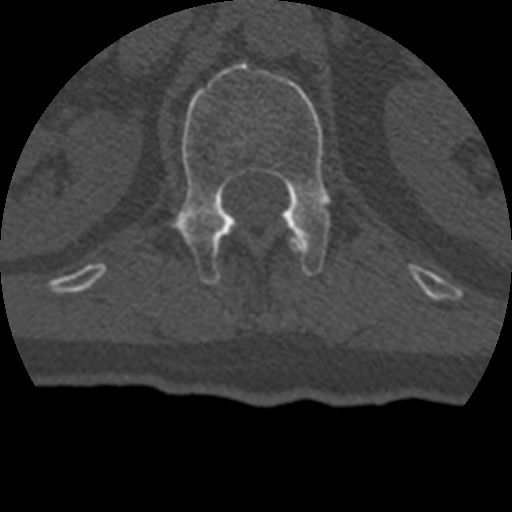
CT including the spine, one axial slice; slice 153 of 399 in the series (ordered by position); reconstruction kernel STANDARD; 120 kVp; bone window (W 1800 / L 400 HU); 1.25 mm slice thickness; 512 × 512 image matrix, field of view 160 × 160 mm. Patient age 69 years. Case-level facts recorded for this patient, not image findings: primary cancer: prostate.
Structures marked on this image (semi-automatic segmentation, software-assisted and operator-edited):
- L1 vertebra: bounding box <172,62,331,284> (left, top, right, bottom; pixels)
- T12 vertebra: <289,237,303,252>